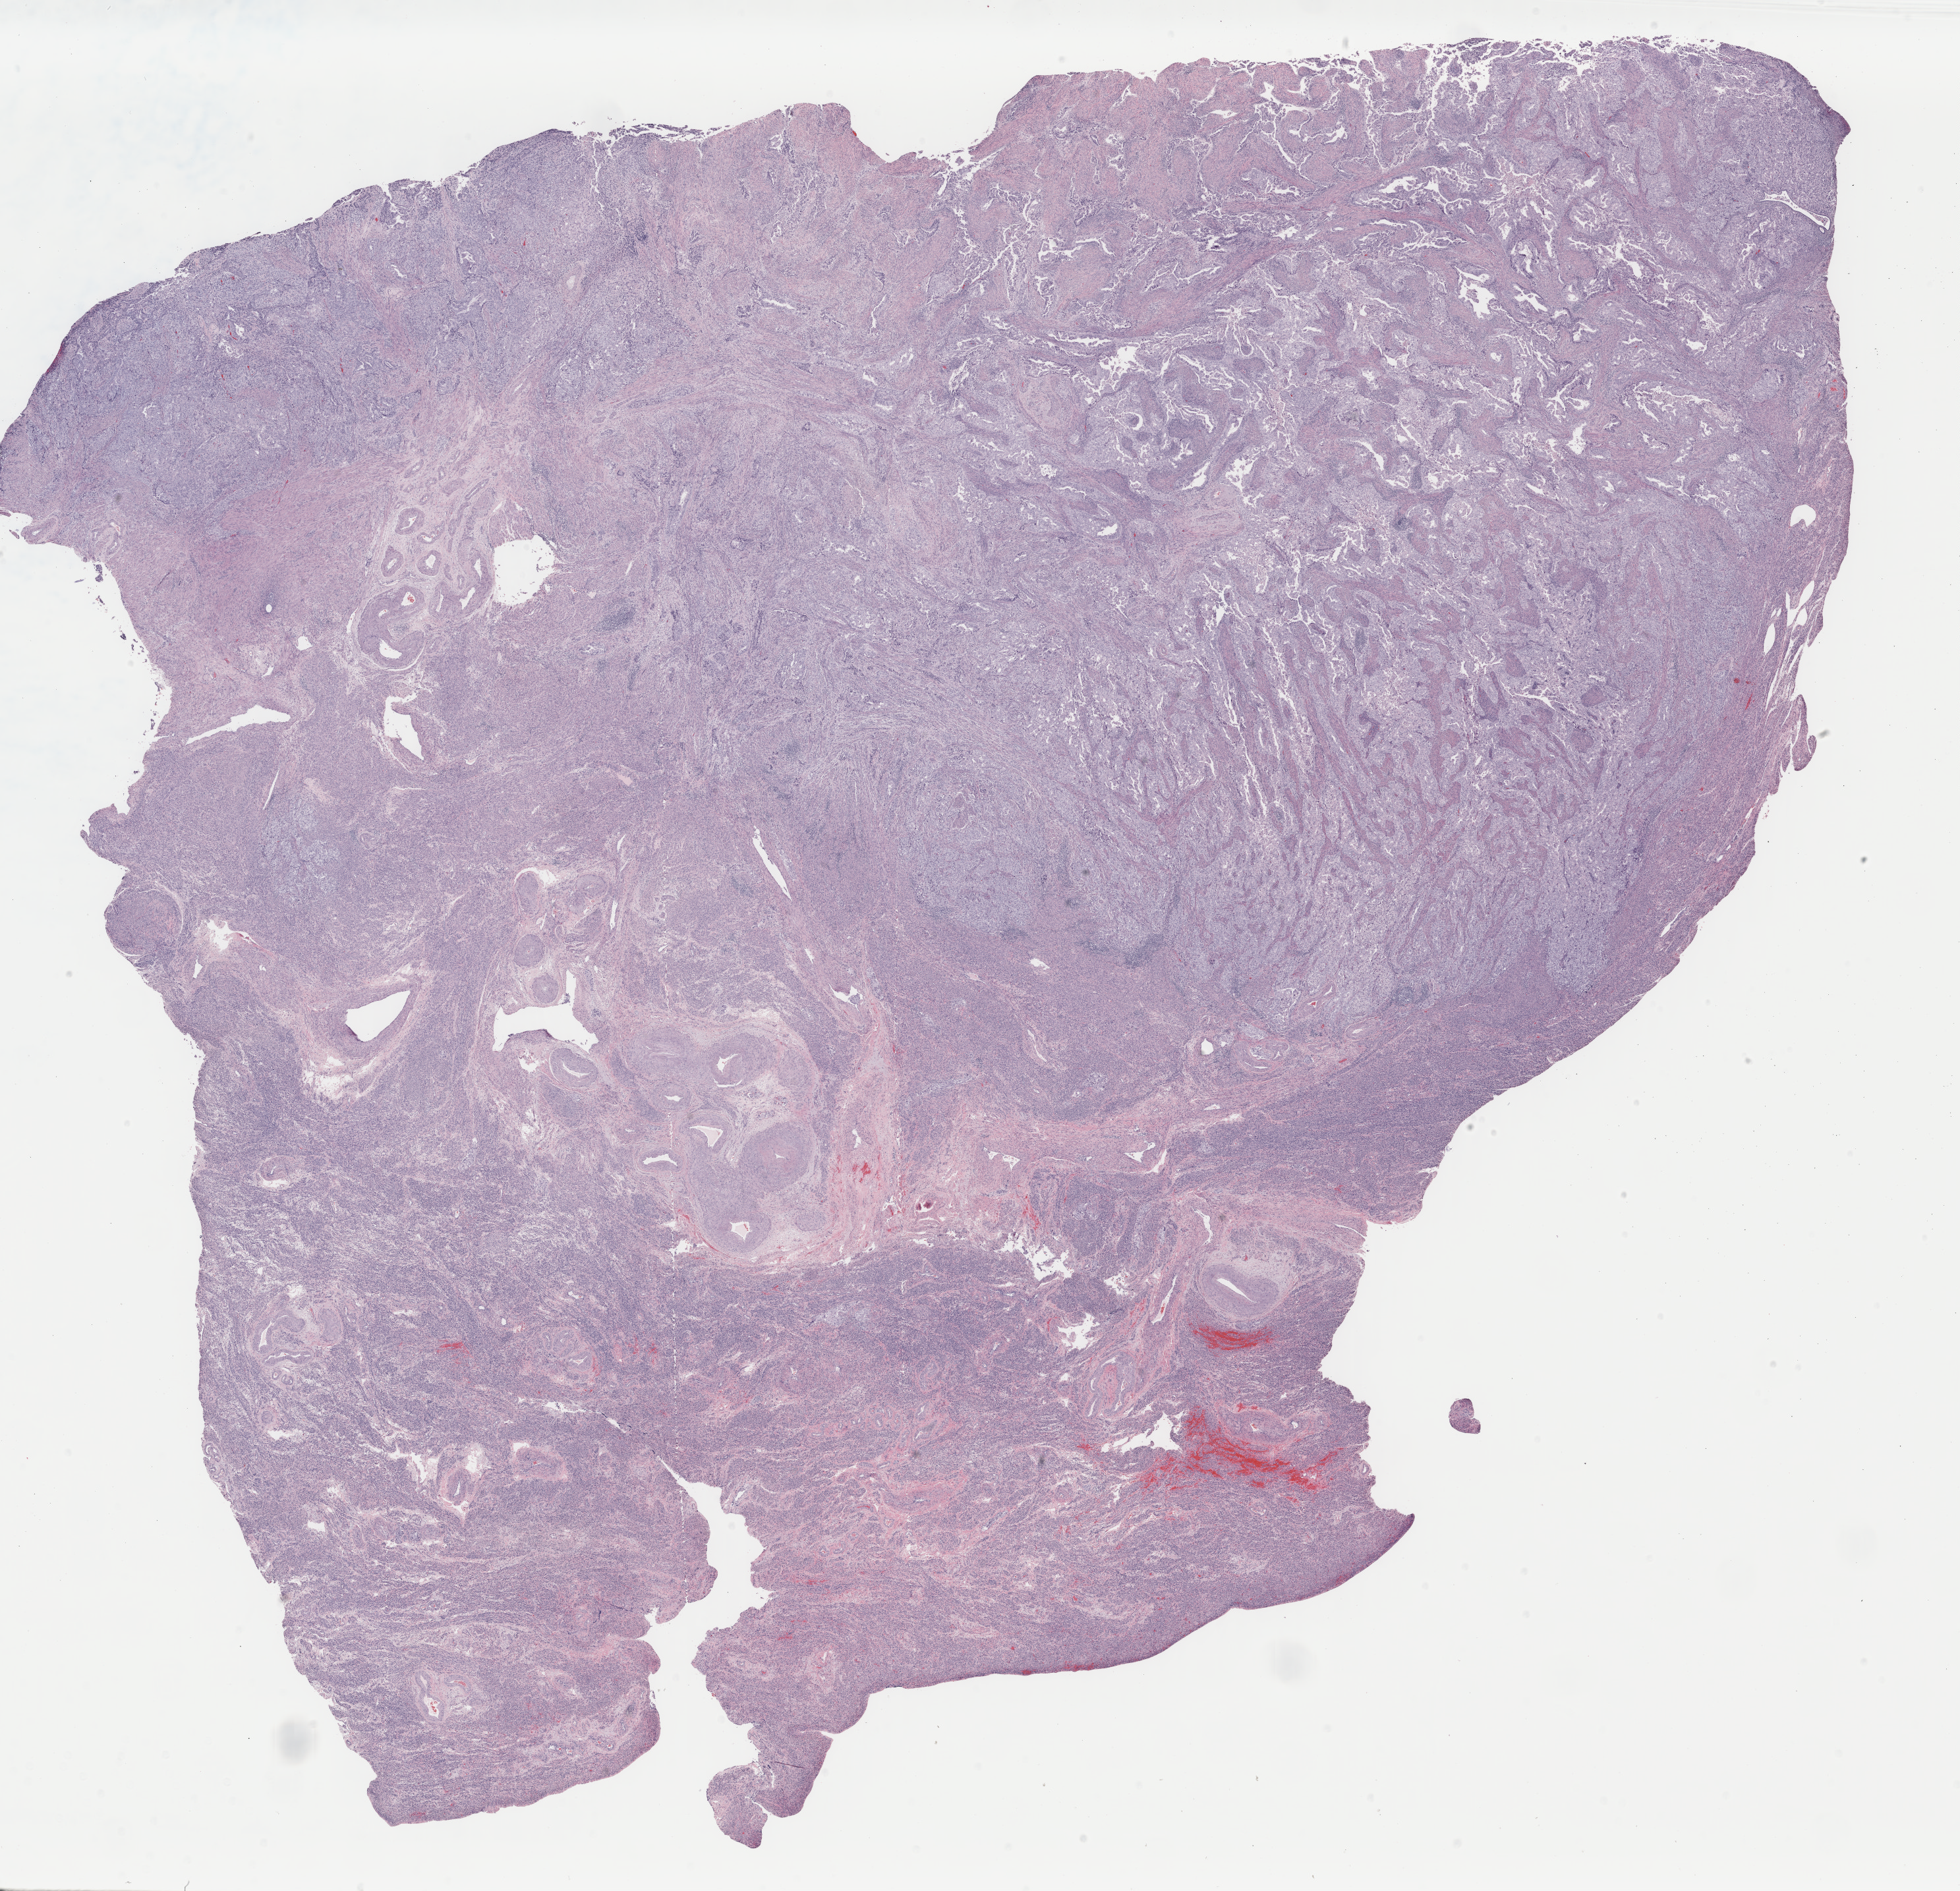
Whole-slide histology image, Hematoxylin and eosin (H&E) stained, whole scanned area (about 23.6 x 22.8 mm, slide scanned at 40x) shown as a low-resolution overview; formalin-fixed paraffin-embedded (FFPE) diagnostic section; sample: primary tumour, uterus. Female patient; age at initial diagnosis 69 years.
FIGO stage: IIIC1. Diagnosis: Mullerian mixed tumor (endometrium).